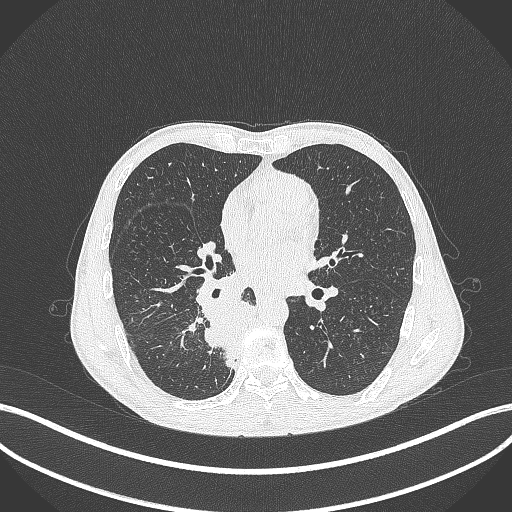
Chest CT, one axial slice. Slice 184 of 371 in the series (ordered by position). 120 kVp. Lung window (W 1500 / L -600 HU). 1 mm slice thickness. 512 × 512 image matrix, field of view 400 × 400 mm. Male patient, age 58 years. From the clinical record (not read from this slice): clinical TNM (as recorded): T3 N1 M1.
Structures marked on this image (bounding box drawn by a radiologist):
- lung tumour (recorded histology: squamous cell carcinoma): bounding box (x1, y1, x2, y2) in pixels: (198, 291, 264, 375)